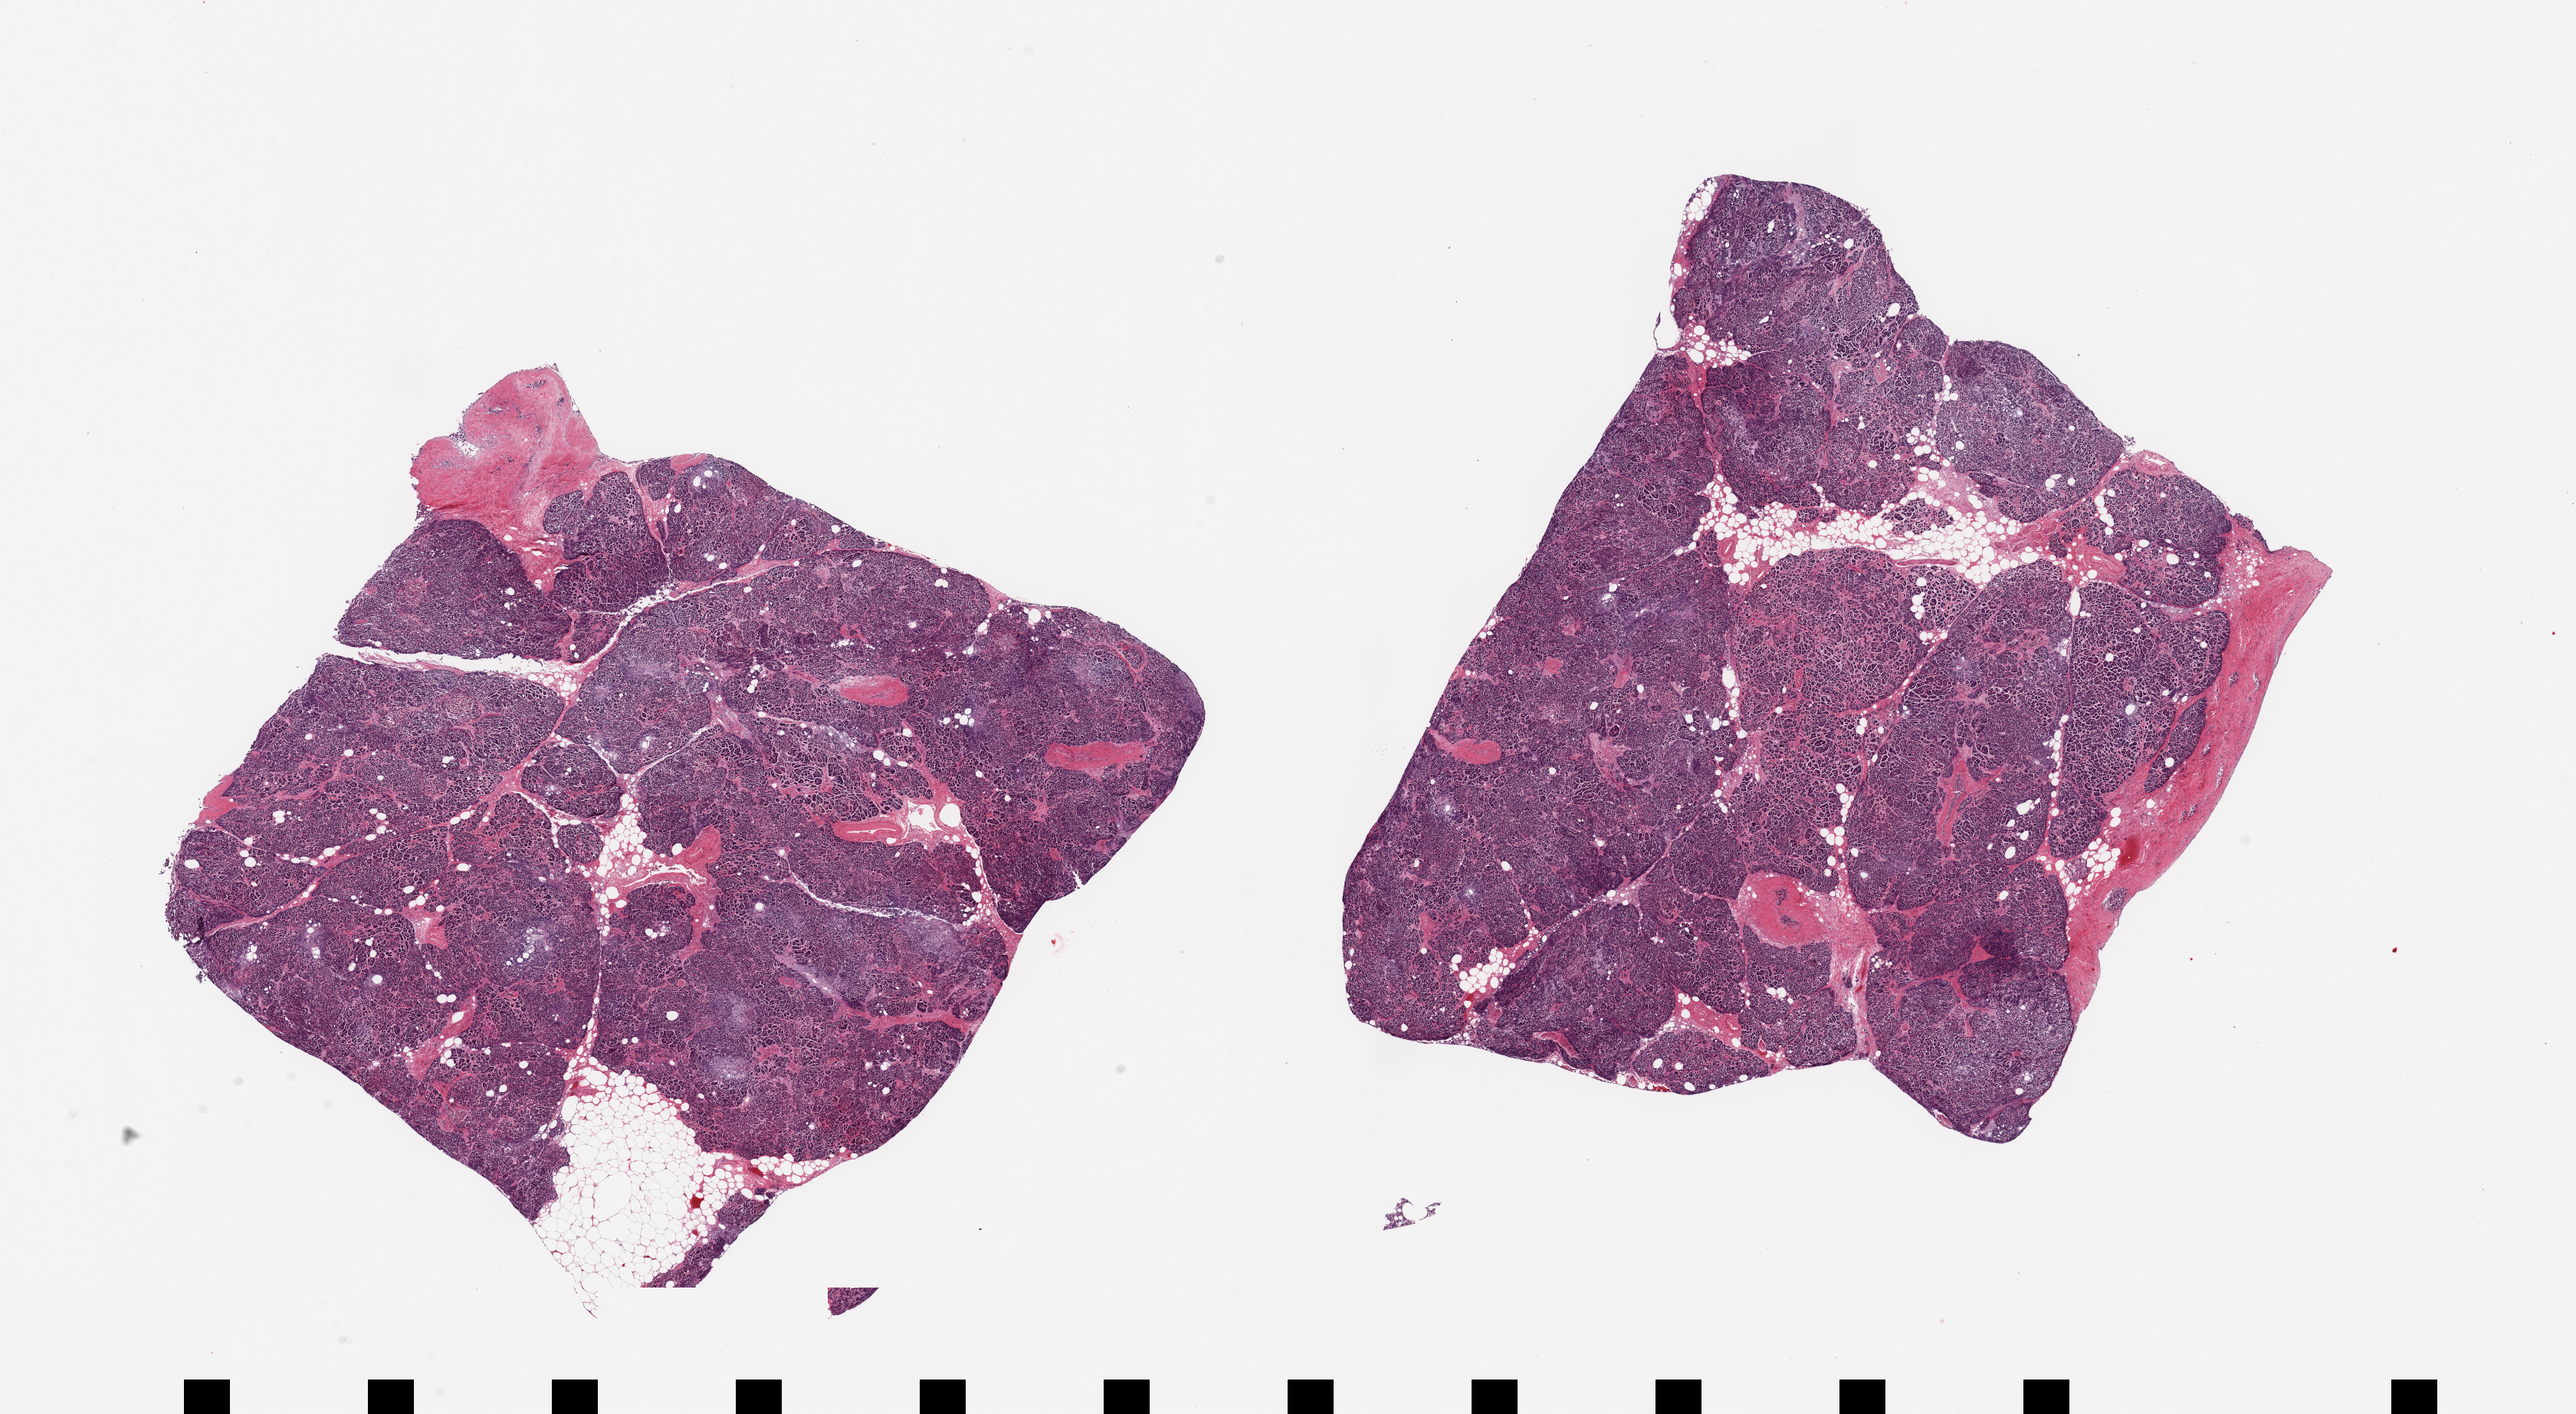
H&E whole-slide image — whole scanned area (about 26.6 x 14.6 mm) shown as a low-resolution overview; PAXgene-fixed paraffin-embedded (PFPE) section; section of pancreas (target tissue); donor tissue sample. Donor: male.
Reviewer comment on this tissue sample: 2 pieces, moderately advanced saponification; Islets degraded.